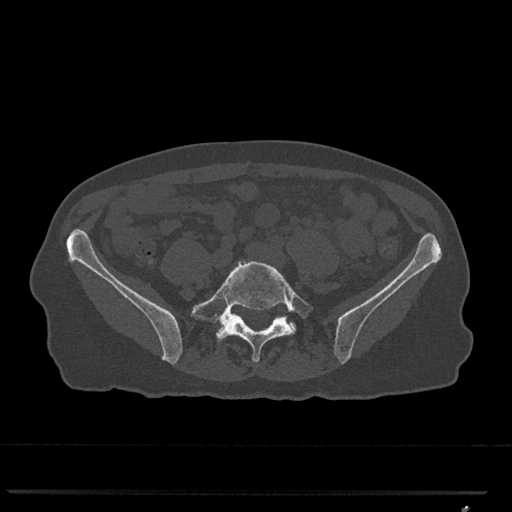
CT including the spine, one axial slice; position 149 of 793 along the scan axis; 120 kVp; bone window (W 1800 / L 400 HU); 0.5 mm slice thickness; 512 × 512 image matrix, field of view 380 × 380 mm. Patient: female, 62 years. From the clinical record (not read from this slice): primary cancer: renal.
Annotated regions visible in this slice (semi-automatic segmentation, software-assisted and operator-edited):
- L5 vertebra: bounding box <191,260,314,362> (left, top, right, bottom; pixels)